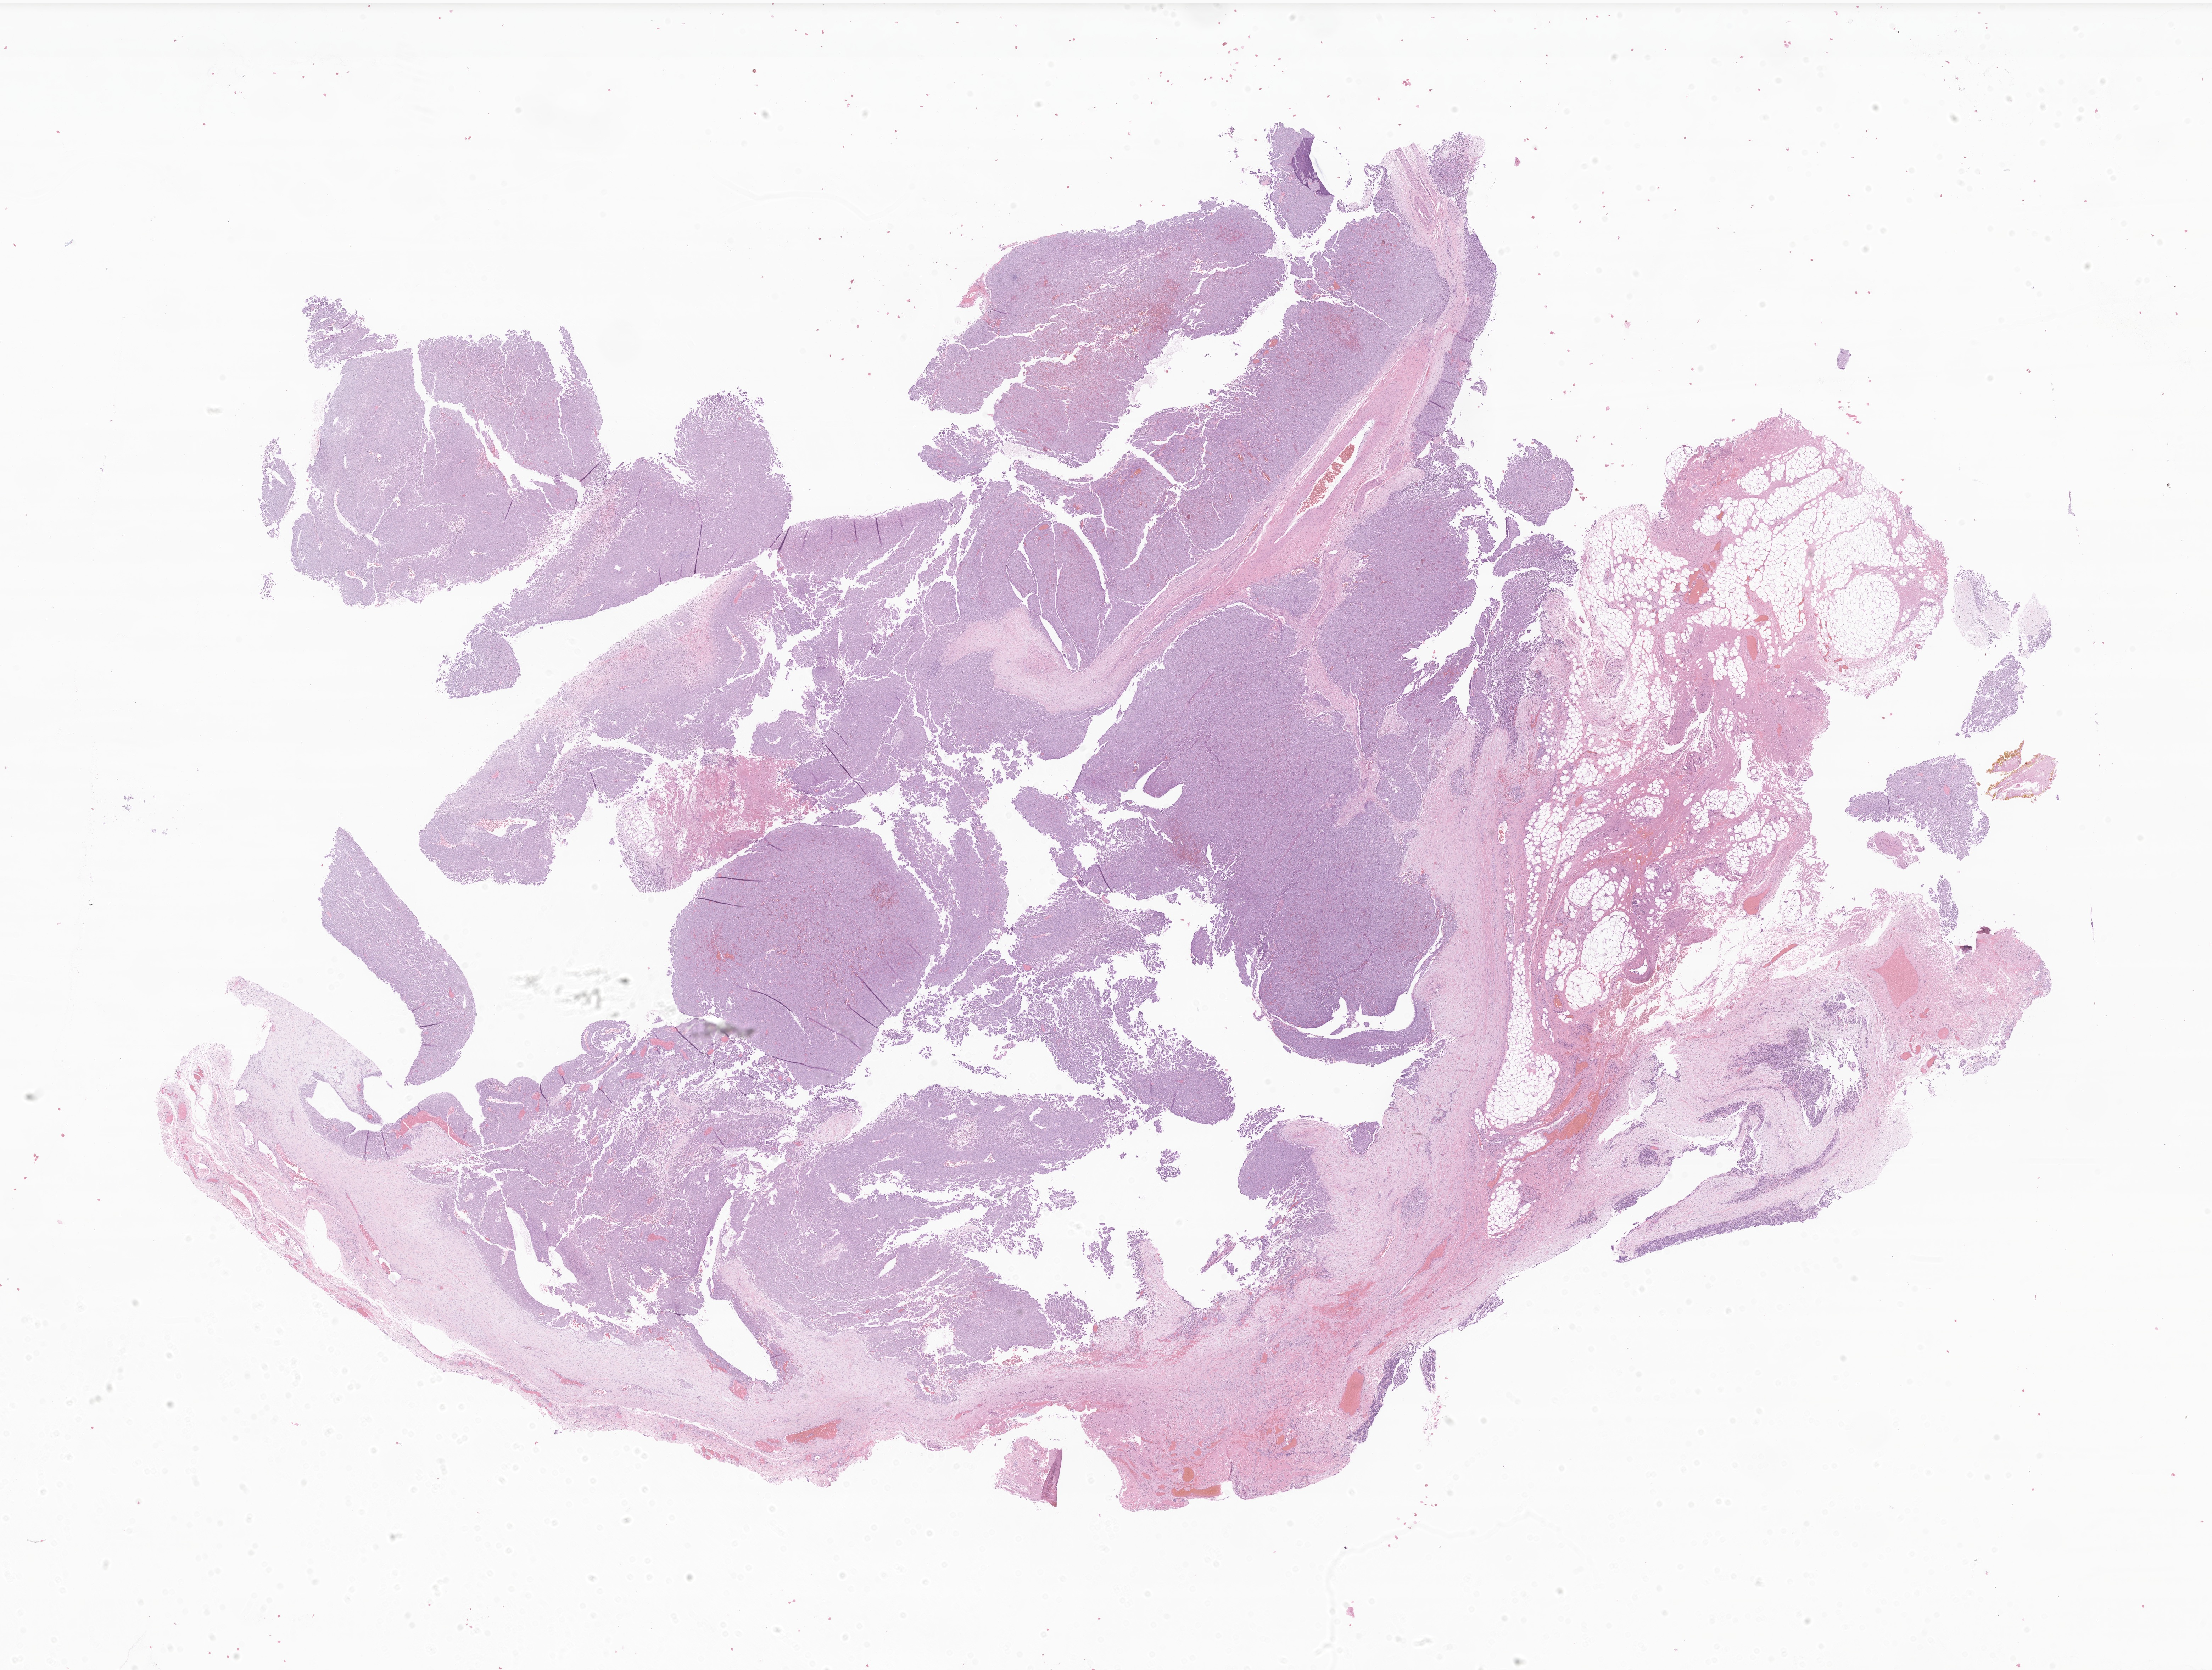
Whole-slide image, haematoxylin and eosin stain of tumor tissue from the cranial and/or facial bone — shown as a low-resolution overview of the whole scanned area (about 26.3 x 19.9 mm), FFPE section. Male patient, age 283 days.
Diagnosis: Undifferentiated sarcoma.